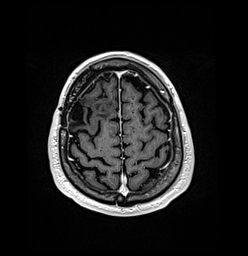
Brain MRI from a brain-tumour surgery series, one axial slice. Slice 33 of 176 in the series (ordered by position). T1-weighted post-contrast. 1 mm slice thickness. 248 × 256 image matrix. From the clinical record (not read from this slice): histopathology: Oligodendroglioma; WHO grade: 3; IDH mutation: yes.
Structures marked on this image (manually delineated by an expert):
- previous resection cavity: bounding box (x1, y1, x2, y2) in pixels: (70, 101, 85, 124)